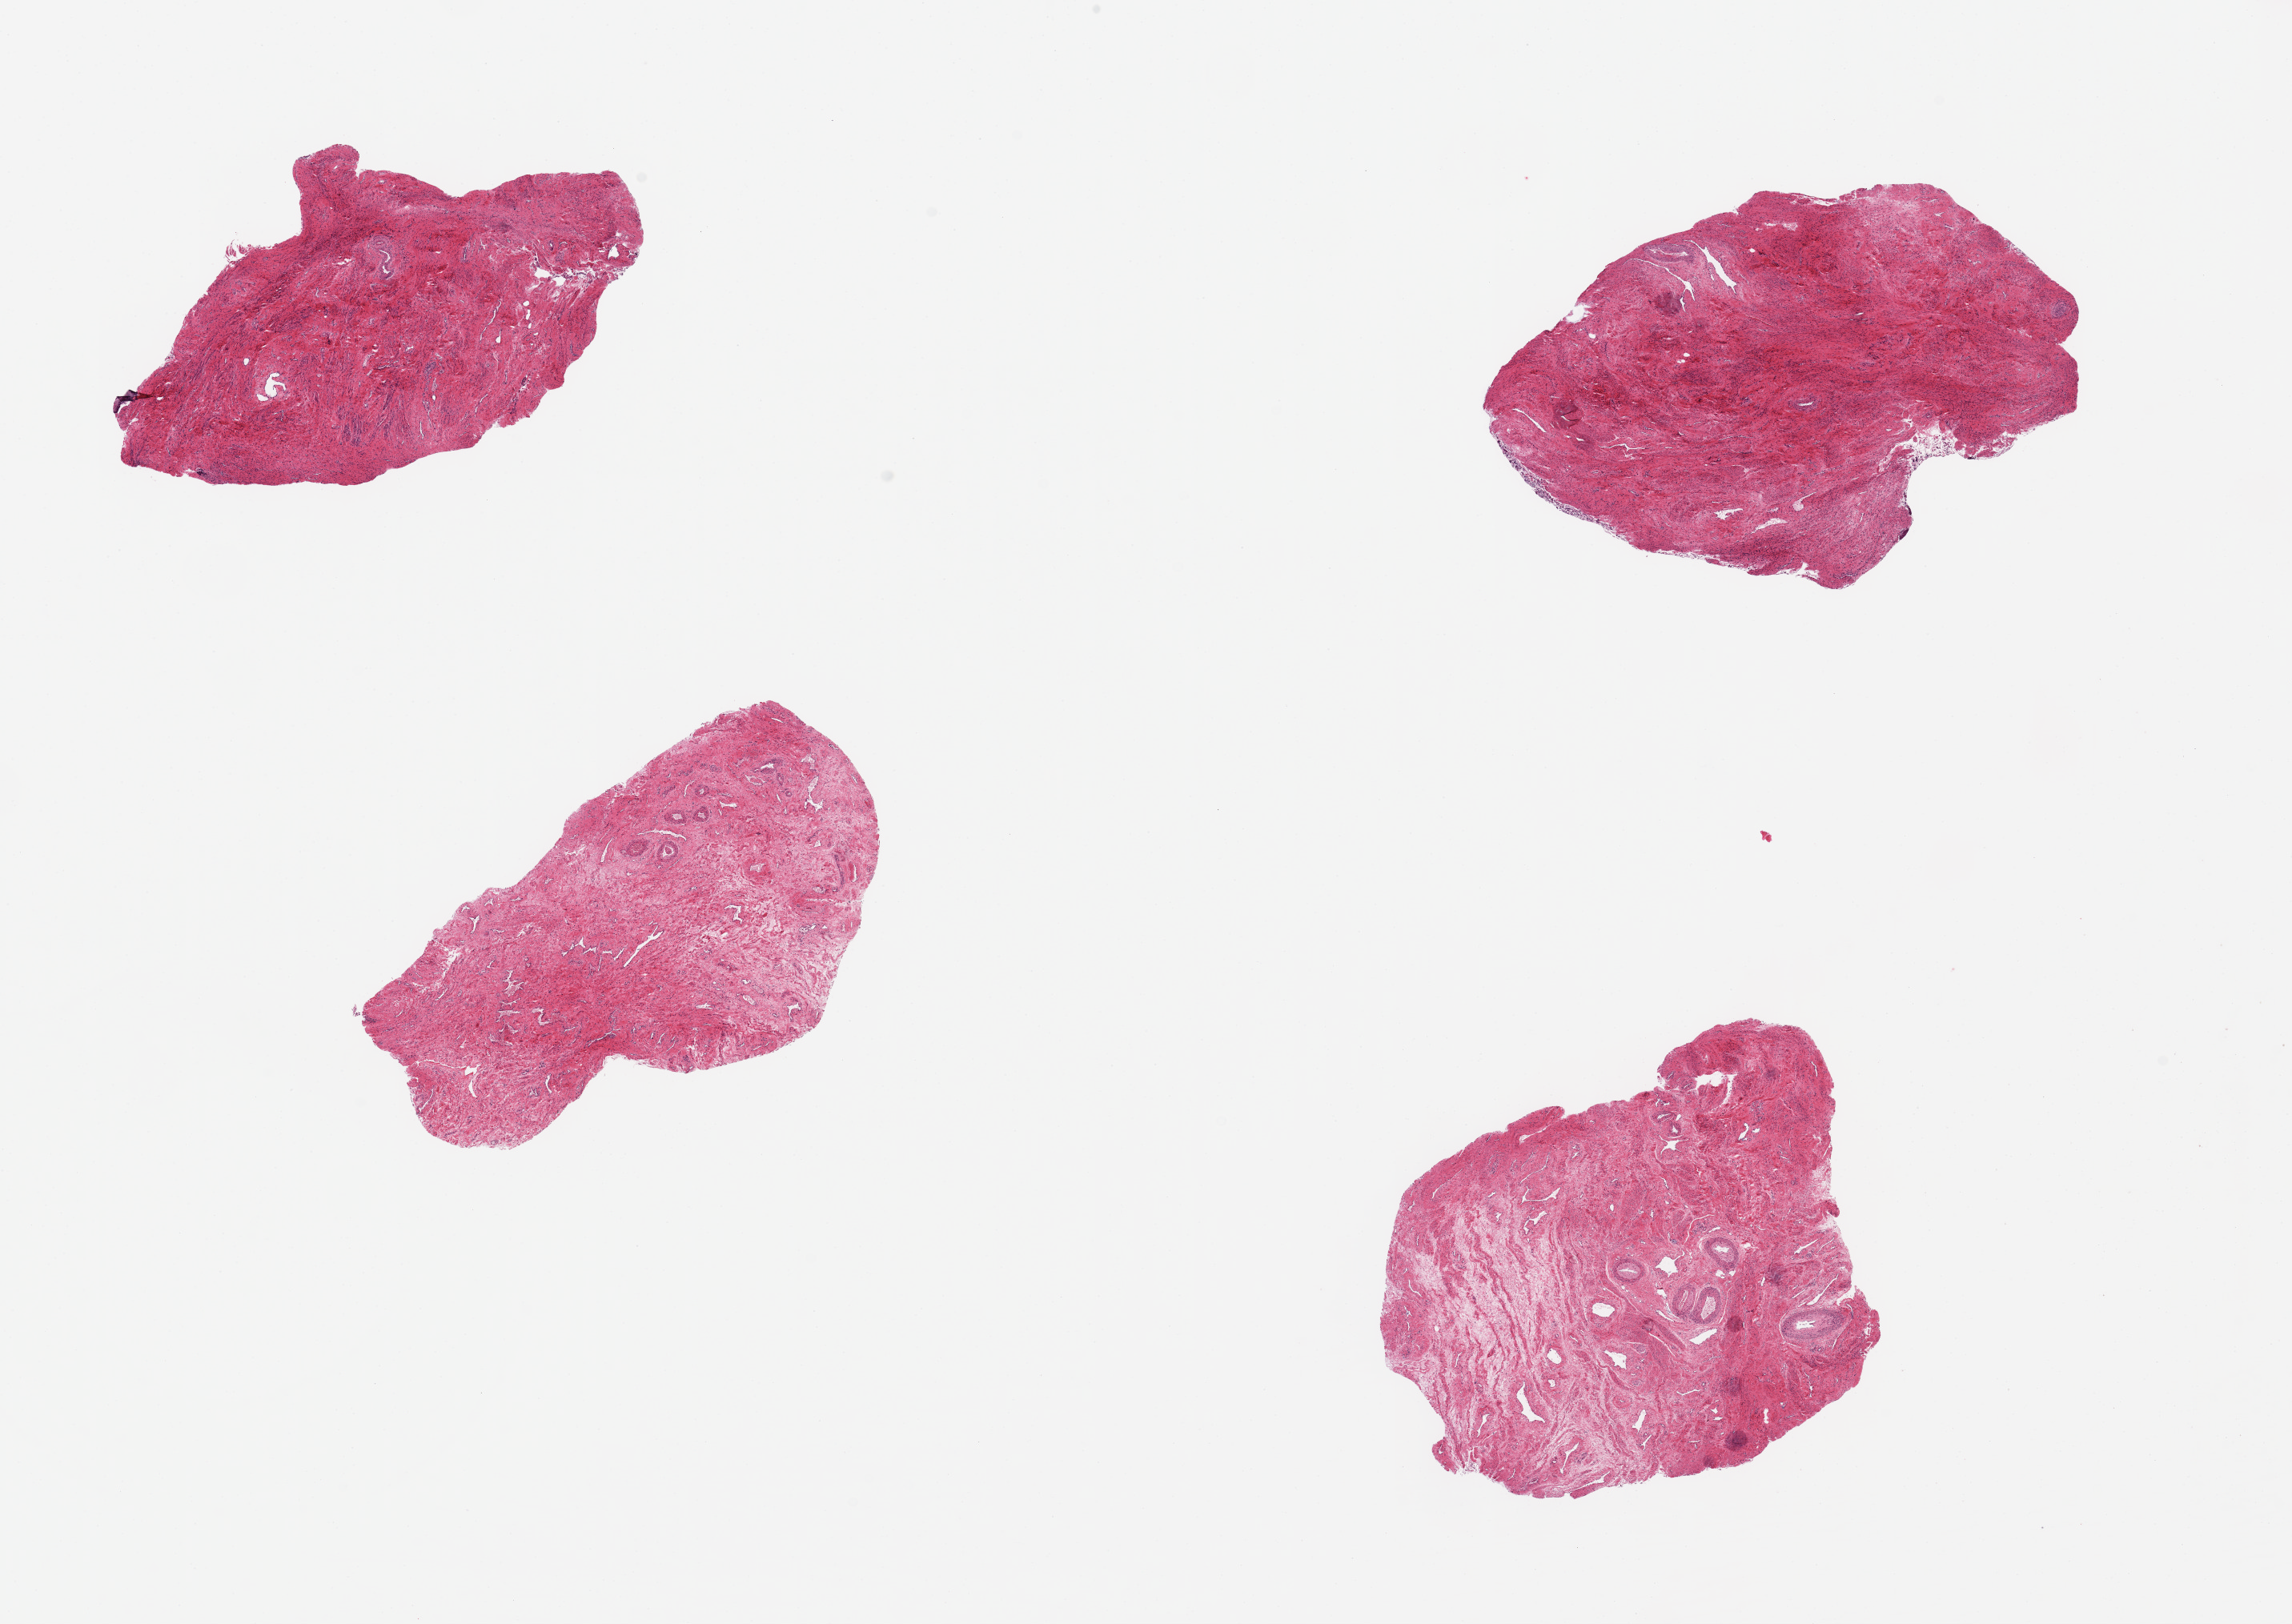
Whole-slide image, H&E stain, shown as a low-resolution overview of the whole scanned area (about 22.6 x 16.0 mm), PAXgene-fixed, paraffin-embedded tissue, sampled site (target tissue): exocervix, tissue donor sample. Donor: female.
• reviewer comment on this tissue sample: 4 ~5x3 mm pieces of fibromuscular stroma with virtually no epithelium